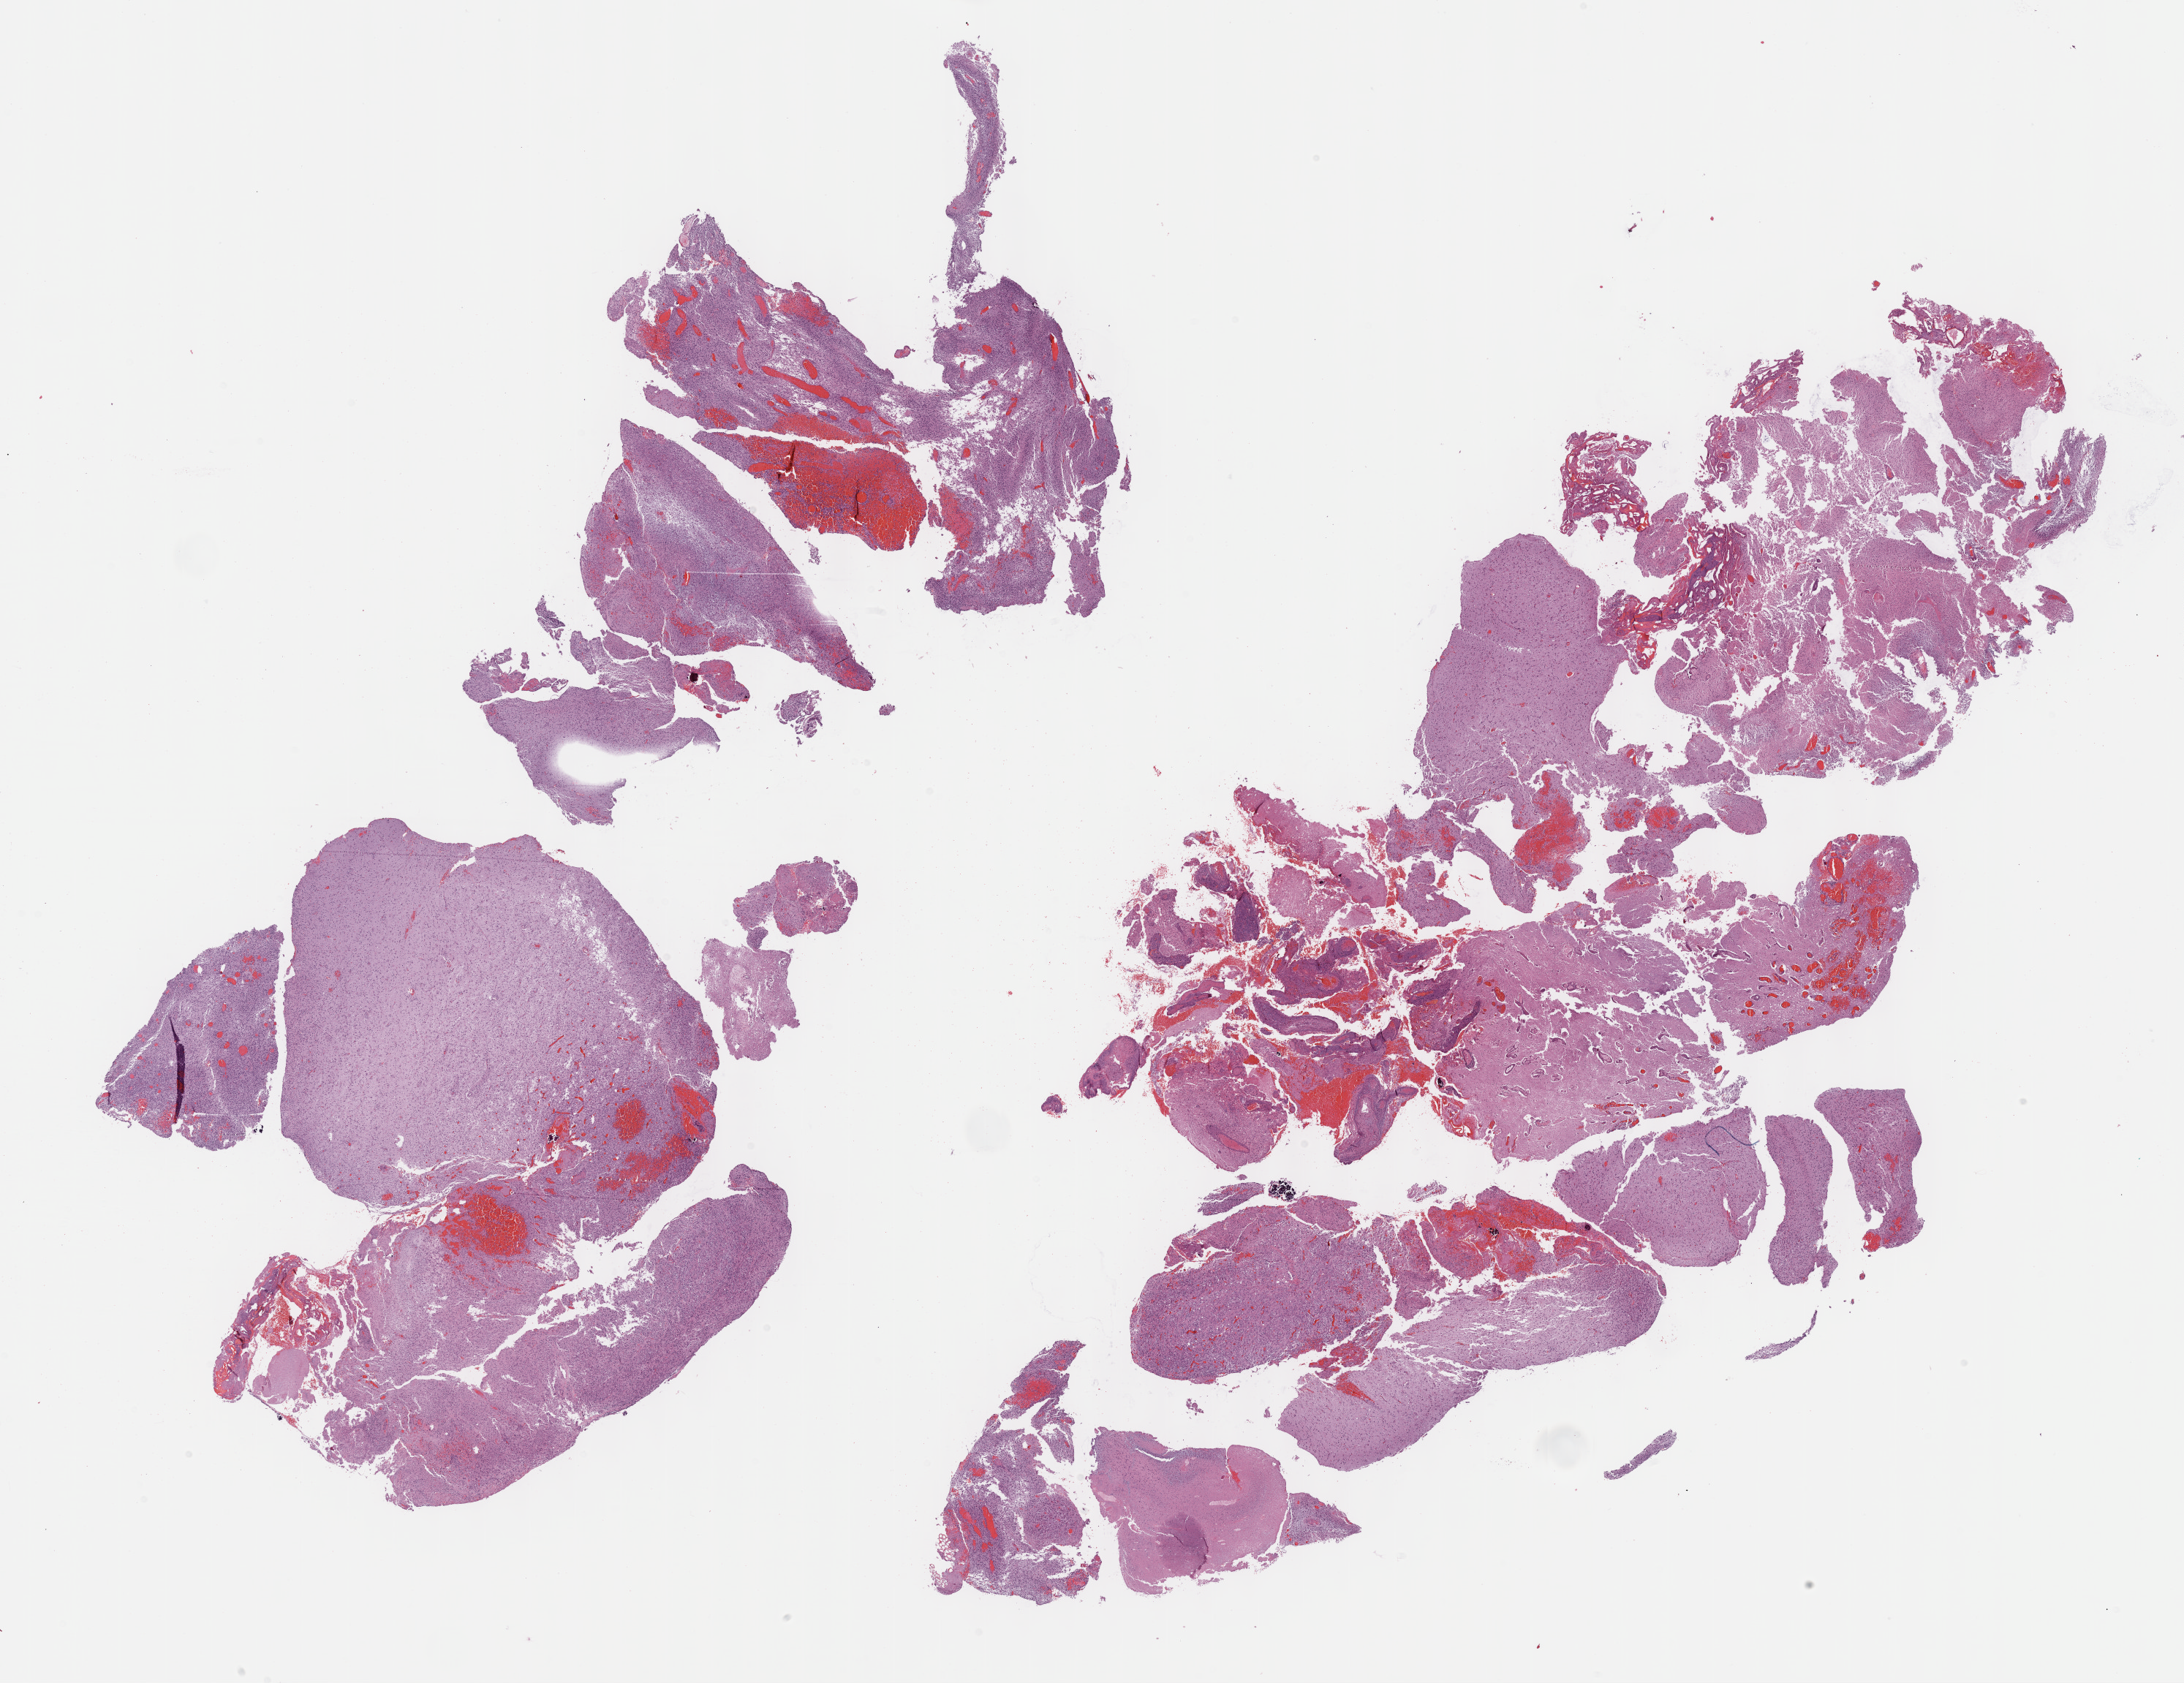
Digitized Hematoxylin and eosin (H&E) stained tissue section (whole slide), low-resolution overview of the scanned area, about 24.2 x 18.6 mm (acquisition: 40x scan), formalin-fixed paraffin-embedded (FFPE) diagnostic section, brain, primary tumour sample. Patient: male, age at initial diagnosis 55 years.
Histologic diagnosis: Glioblastoma (temporal lobe).